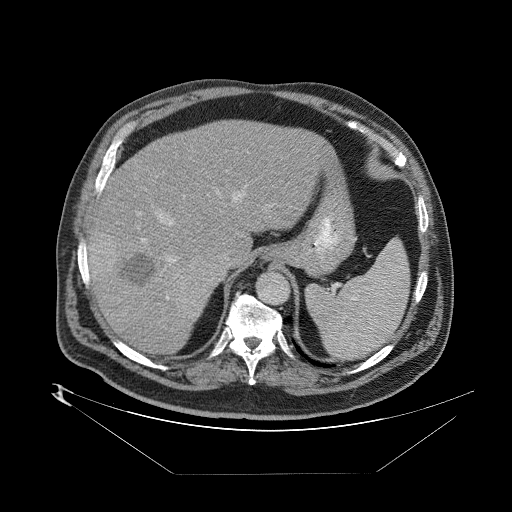
Contrast-enhanced abdominal CT (liver protocol), one axial slice; slice 60 of 89 in the series (ordered by position); one of 2 acquisitions stored at this slice position; soft-tissue window (W 400 / L 40 HU); 2.5 mm slice thickness; 512 × 512 image matrix, field of view 480 × 480 mm. From the clinical record (not read from this slice): diagnosis: hepatocellular carcinoma (patient treated with transarterial chemoembolisation; whether this scan precedes or follows treatment is not stated here); TNM stage (as recorded): Stage-II; Child-Pugh class: B; tumour differentiation: moderately differentiated; tumour nodularity: multinodular.
Annotated regions visible in this slice (semi-automatic segmentation, software-assisted and operator-edited):
- abdominal aorta: bounding box <257,272,289,305> (left, top, right, bottom; pixels)
- liver parenchyma outside the tumour (the mass and vessels are separate outlines, so this box may not span the whole liver): <88,118,326,353>
- mass: <91,232,218,319>
- liver vessels: <89,195,288,323>